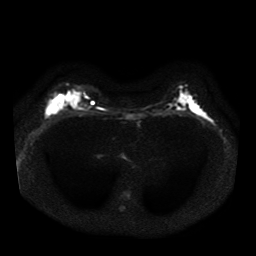
Breast MRI, one axial slice. Position 24 of 41 along the scan axis. Diffusion-weighted series; image 2 of 4 stored at this slice position (different b-values; order by instance number). 1.5 T. 5 mm slice thickness. 256 × 256 image matrix, field of view 330 × 330 mm. Female patient.
Outlined on this slice (outlined manually by an expert reader):
- tumour on diffusion-weighted imaging: box from (x=48, y=94) to (x=62, y=112) px